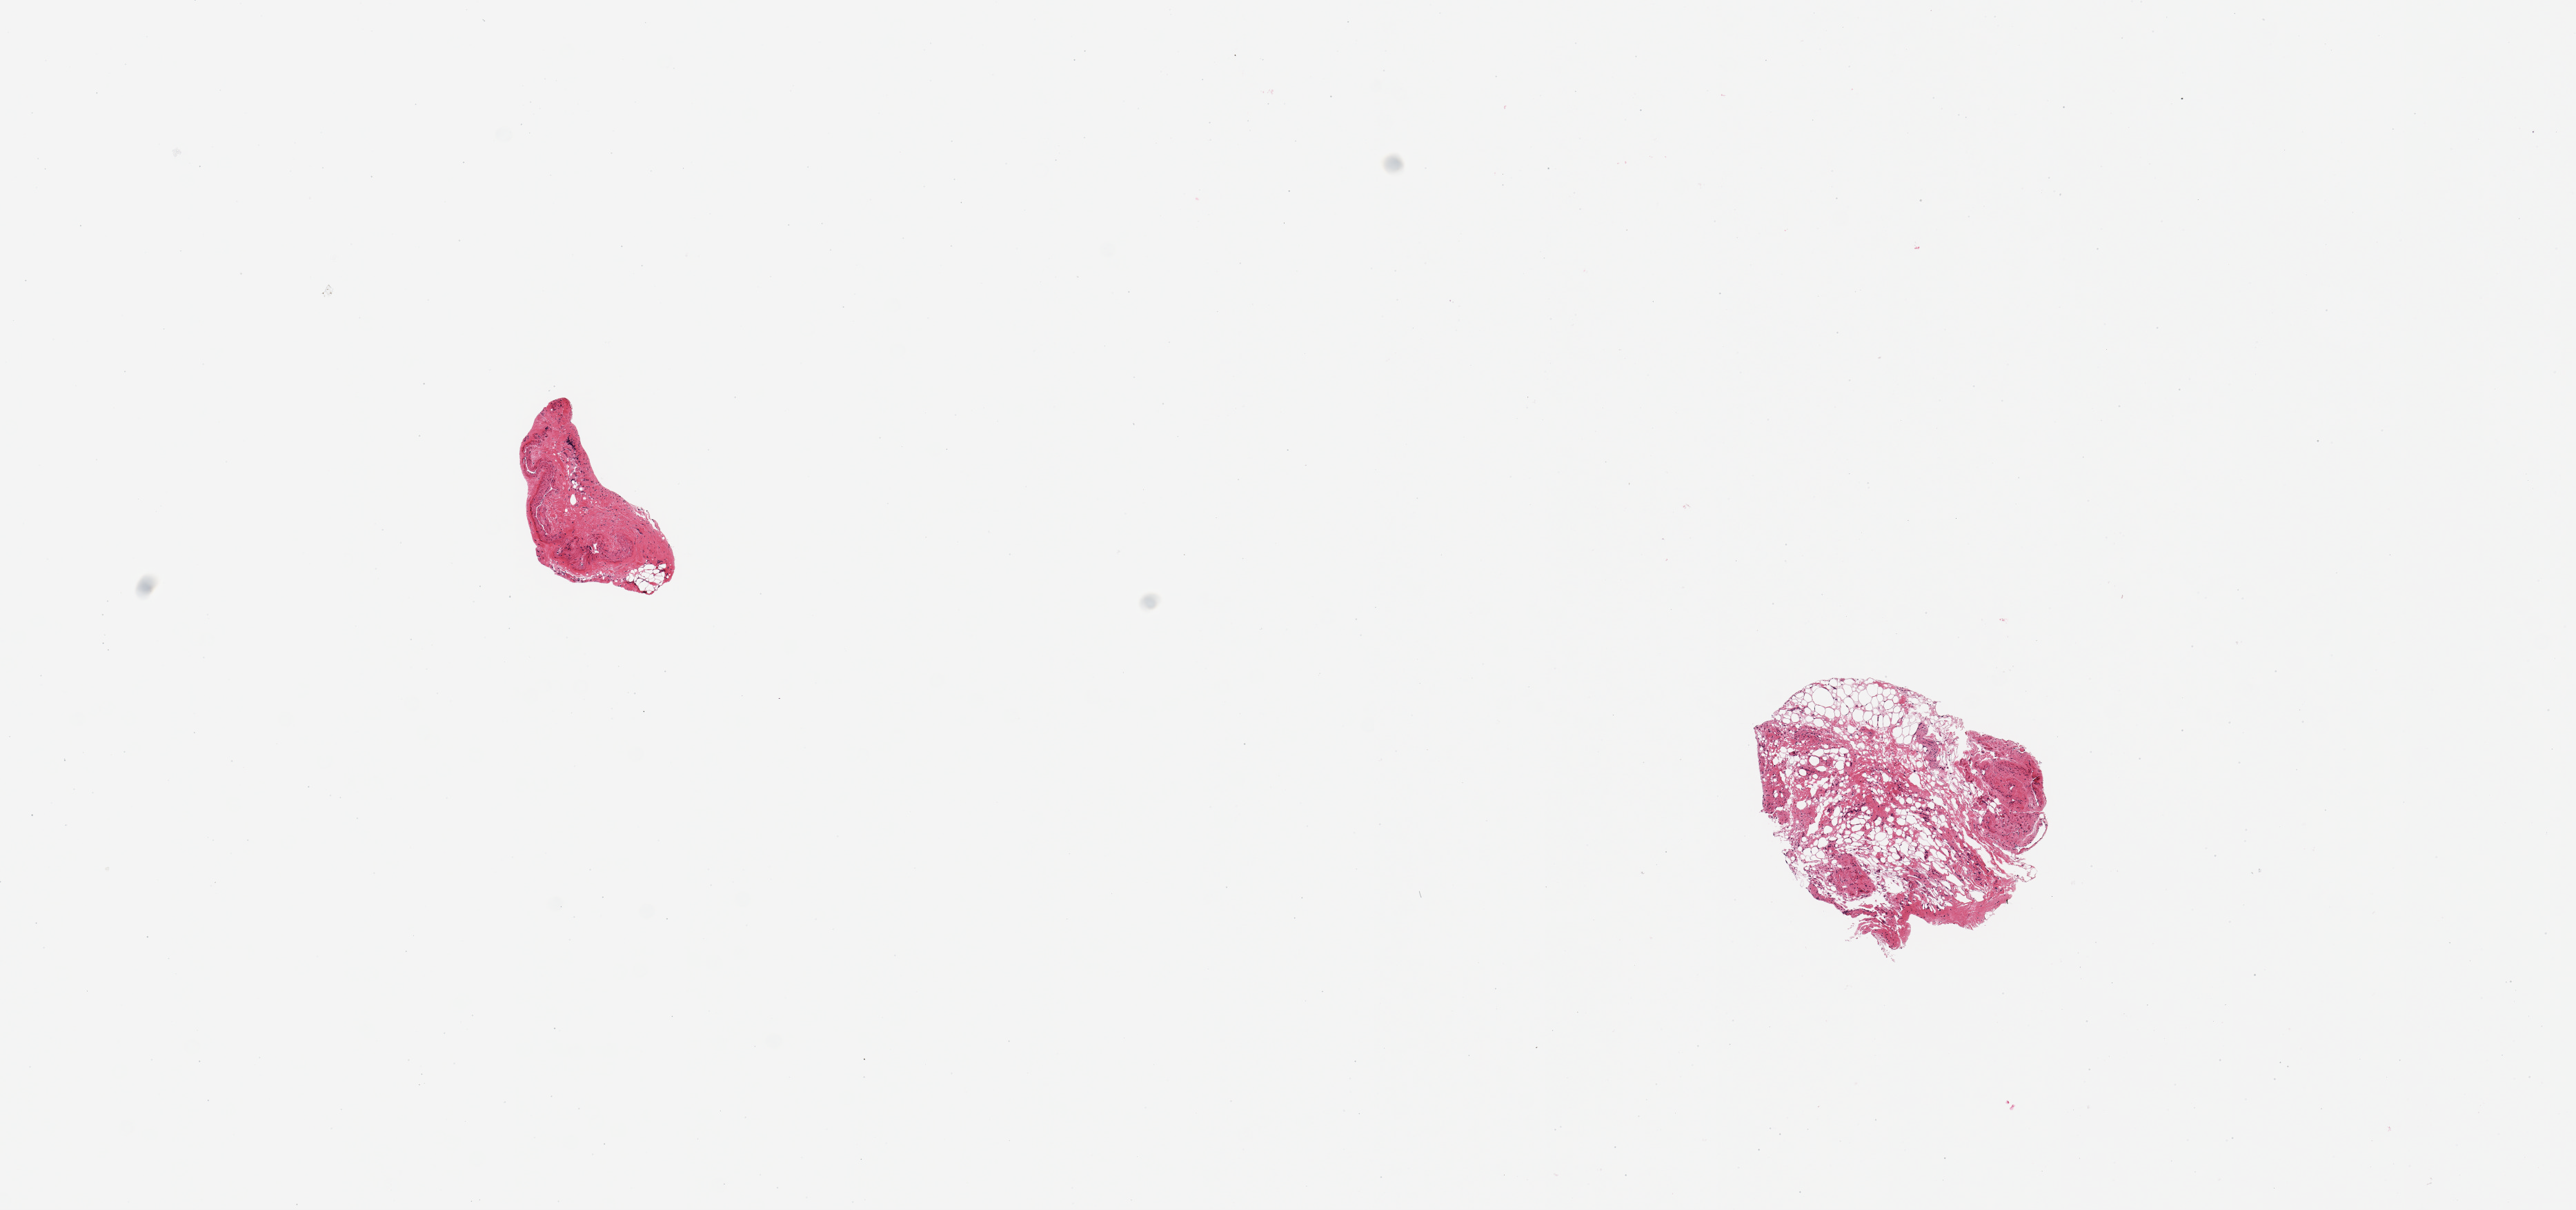
Digitized haematoxylin and eosin-stained section, whole scanned area (about 14.8 x 6.9 mm) shown as a low-resolution overview. PAXgene-fixed, paraffin-embedded tissue. Sampled site (target tissue): coronary artery. Tissue donor sample. Donor sex: male.
- pathologist's review note for this sample: 2 pieces: 1 very small (1mm) group of small arteries; other is 90% fat and a tiny group of small vessels